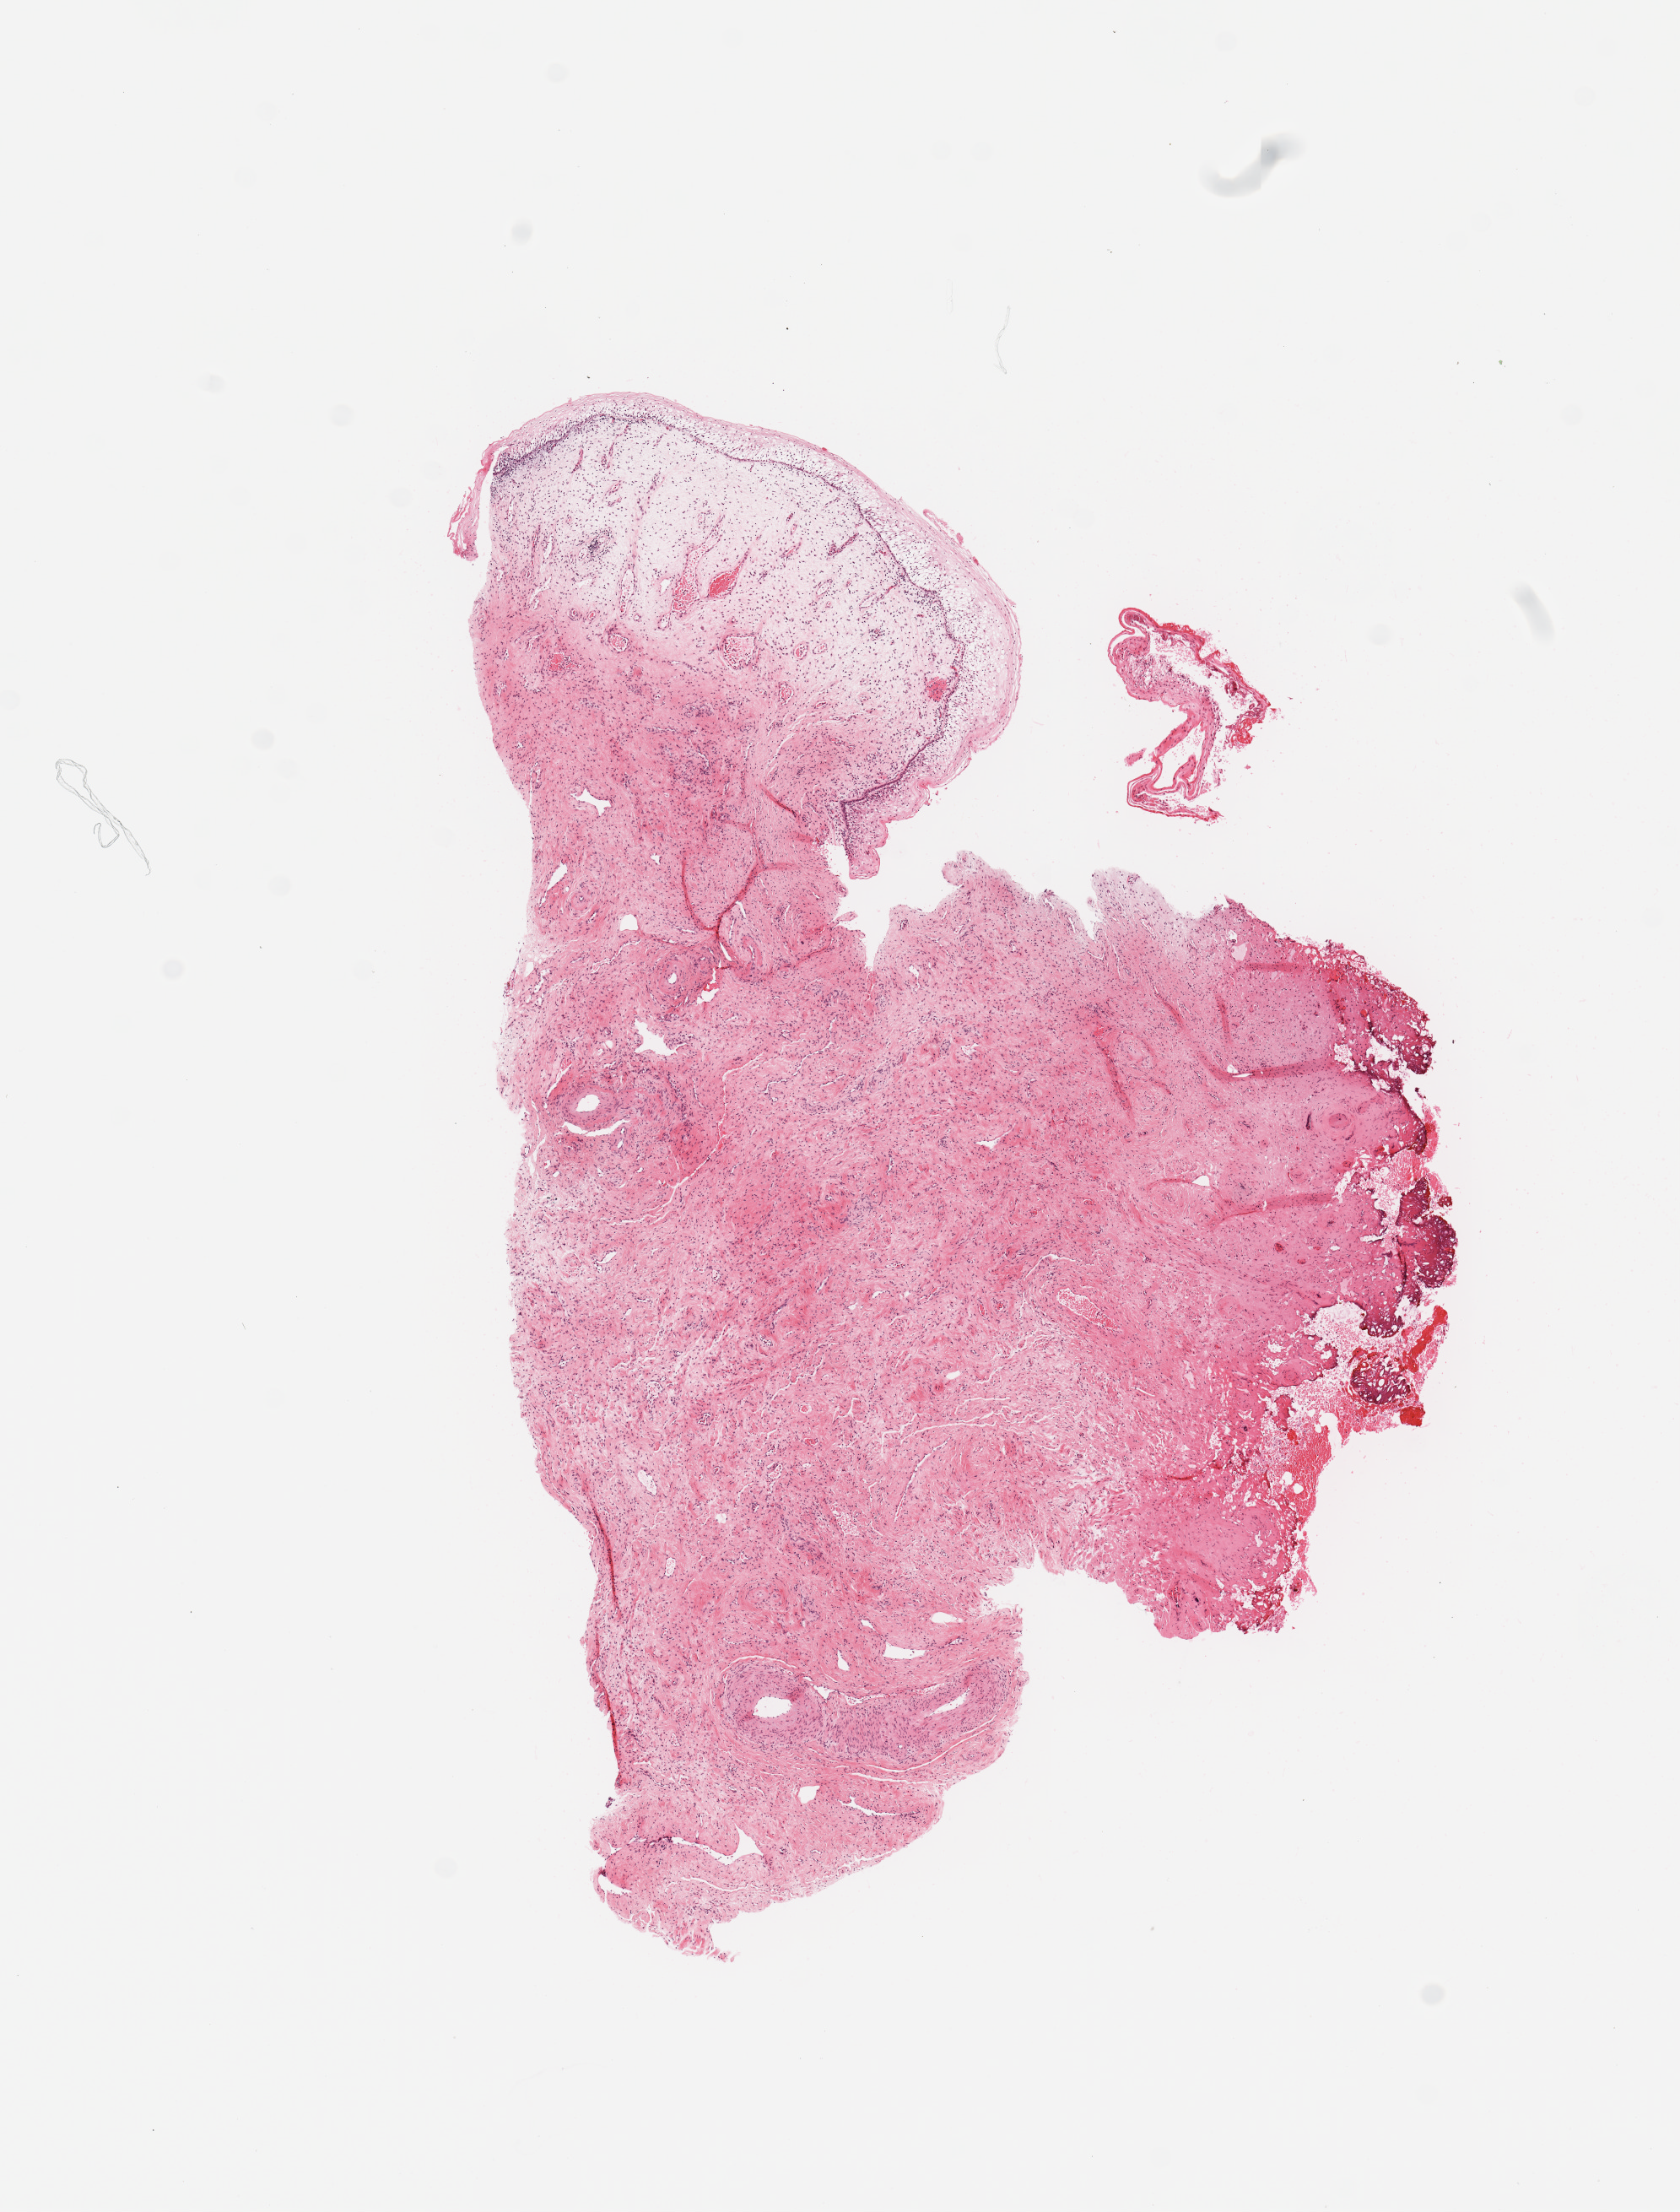
Whole-slide histology image, H&E-stained, whole scanned area (about 7.9 x 10.4 mm) shown as a low-resolution overview; normal (non-tumour) tissue sample, uterus. Patient: female, age 59 years.
This section: normal (non-tumour) tissue from the same patient. Patient diagnosis: Endometrioid adenocarcinoma, NOS.